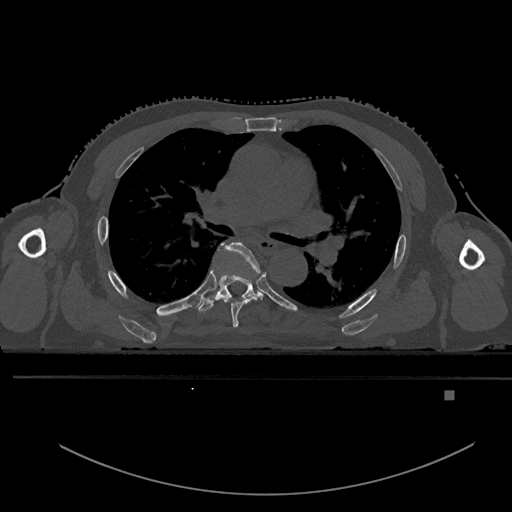
CT including the spine, one axial slice; slice 333 of 969 in the series (ordered by position); bone window (W 1800 / L 400 HU); 0.5 mm slice thickness; 512 × 512 image matrix, field of view 456 × 456 mm. Male patient, age 82 years. Case-level facts recorded for this patient, not image findings: primary cancer: prostate.
Outlined on this slice (semi-automatic segmentation, software-assisted and operator-edited):
- T5 vertebra: bounding box [x1, y1, x2, y2] px = [221, 242, 262, 328]
- T6 vertebra: [195, 245, 261, 312]